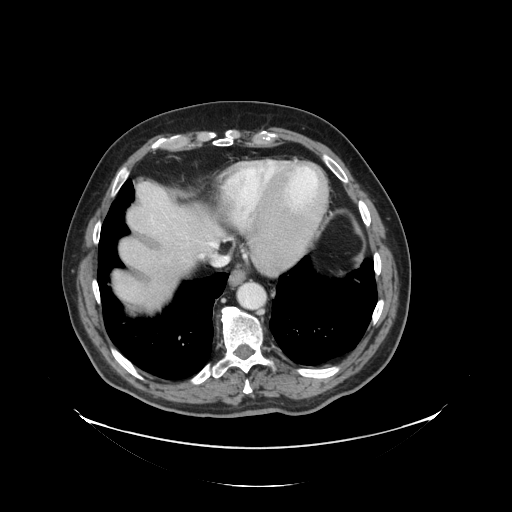
Contrast-enhanced abdominal CT, one axial slice; position 119 of 138 along the scan axis; 120 kVp; intravenous contrast given; soft-tissue window (W 400 / L 40 HU); 2.5 mm slice thickness; 512 × 512 image matrix, field of view 497 × 497 mm. Male patient, age 77 years. Case-level facts recorded for this patient, not image findings: diagnosis: colorectal cancer liver metastases, imaged before liver resection; multiple liver metastases: no; largest metastasis: 1.5 cm; disease in both lobes: no.
Annotated regions visible in this slice (manually delineated by an expert):
- hepatic veins: bounding box [x1, y1, x2, y2] px = [209, 242, 217, 247]
- liver: [113, 183, 222, 311]
- planned liver remnant (the part of the liver to remain after resection): [113, 184, 221, 289]